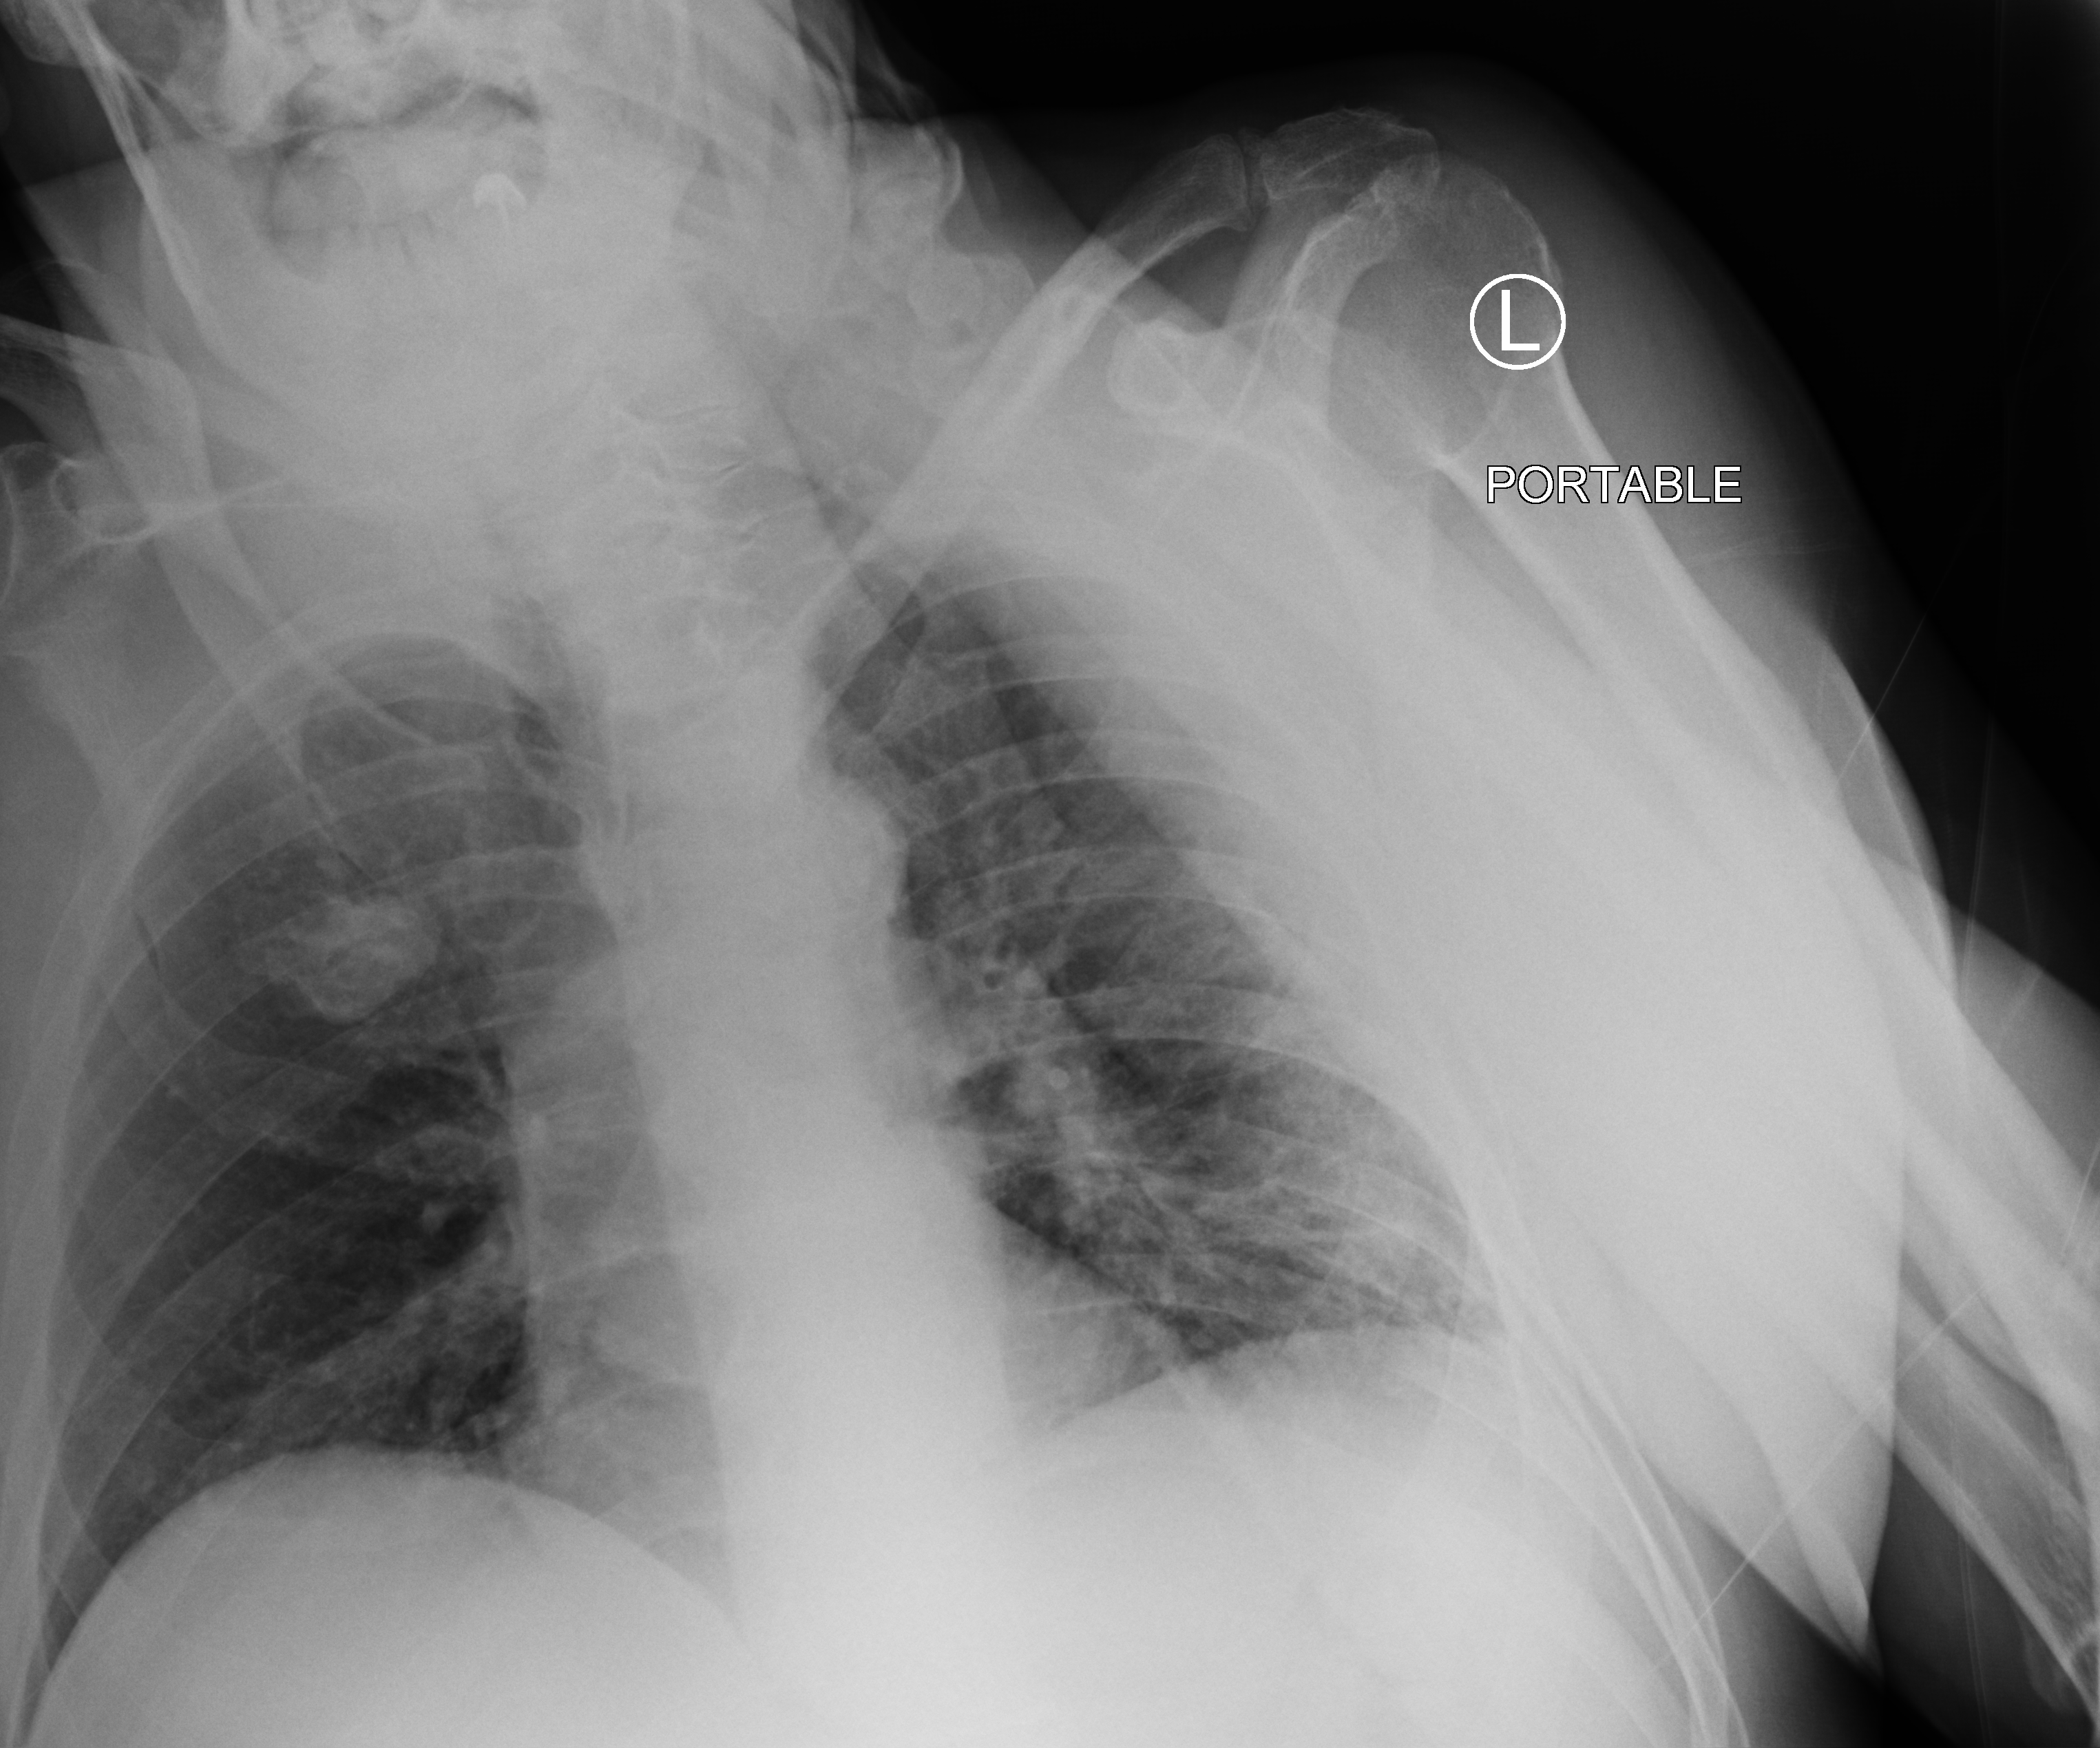
Bedside chest radiograph (computed radiography); anteroposterior (AP) projection. Male patient hospitalised with COVID-19, age 75–90 years.
From the hospital-stay record, not from the radiograph (when in the stay this image was taken is not recorded): hypertension (admission record): yes.